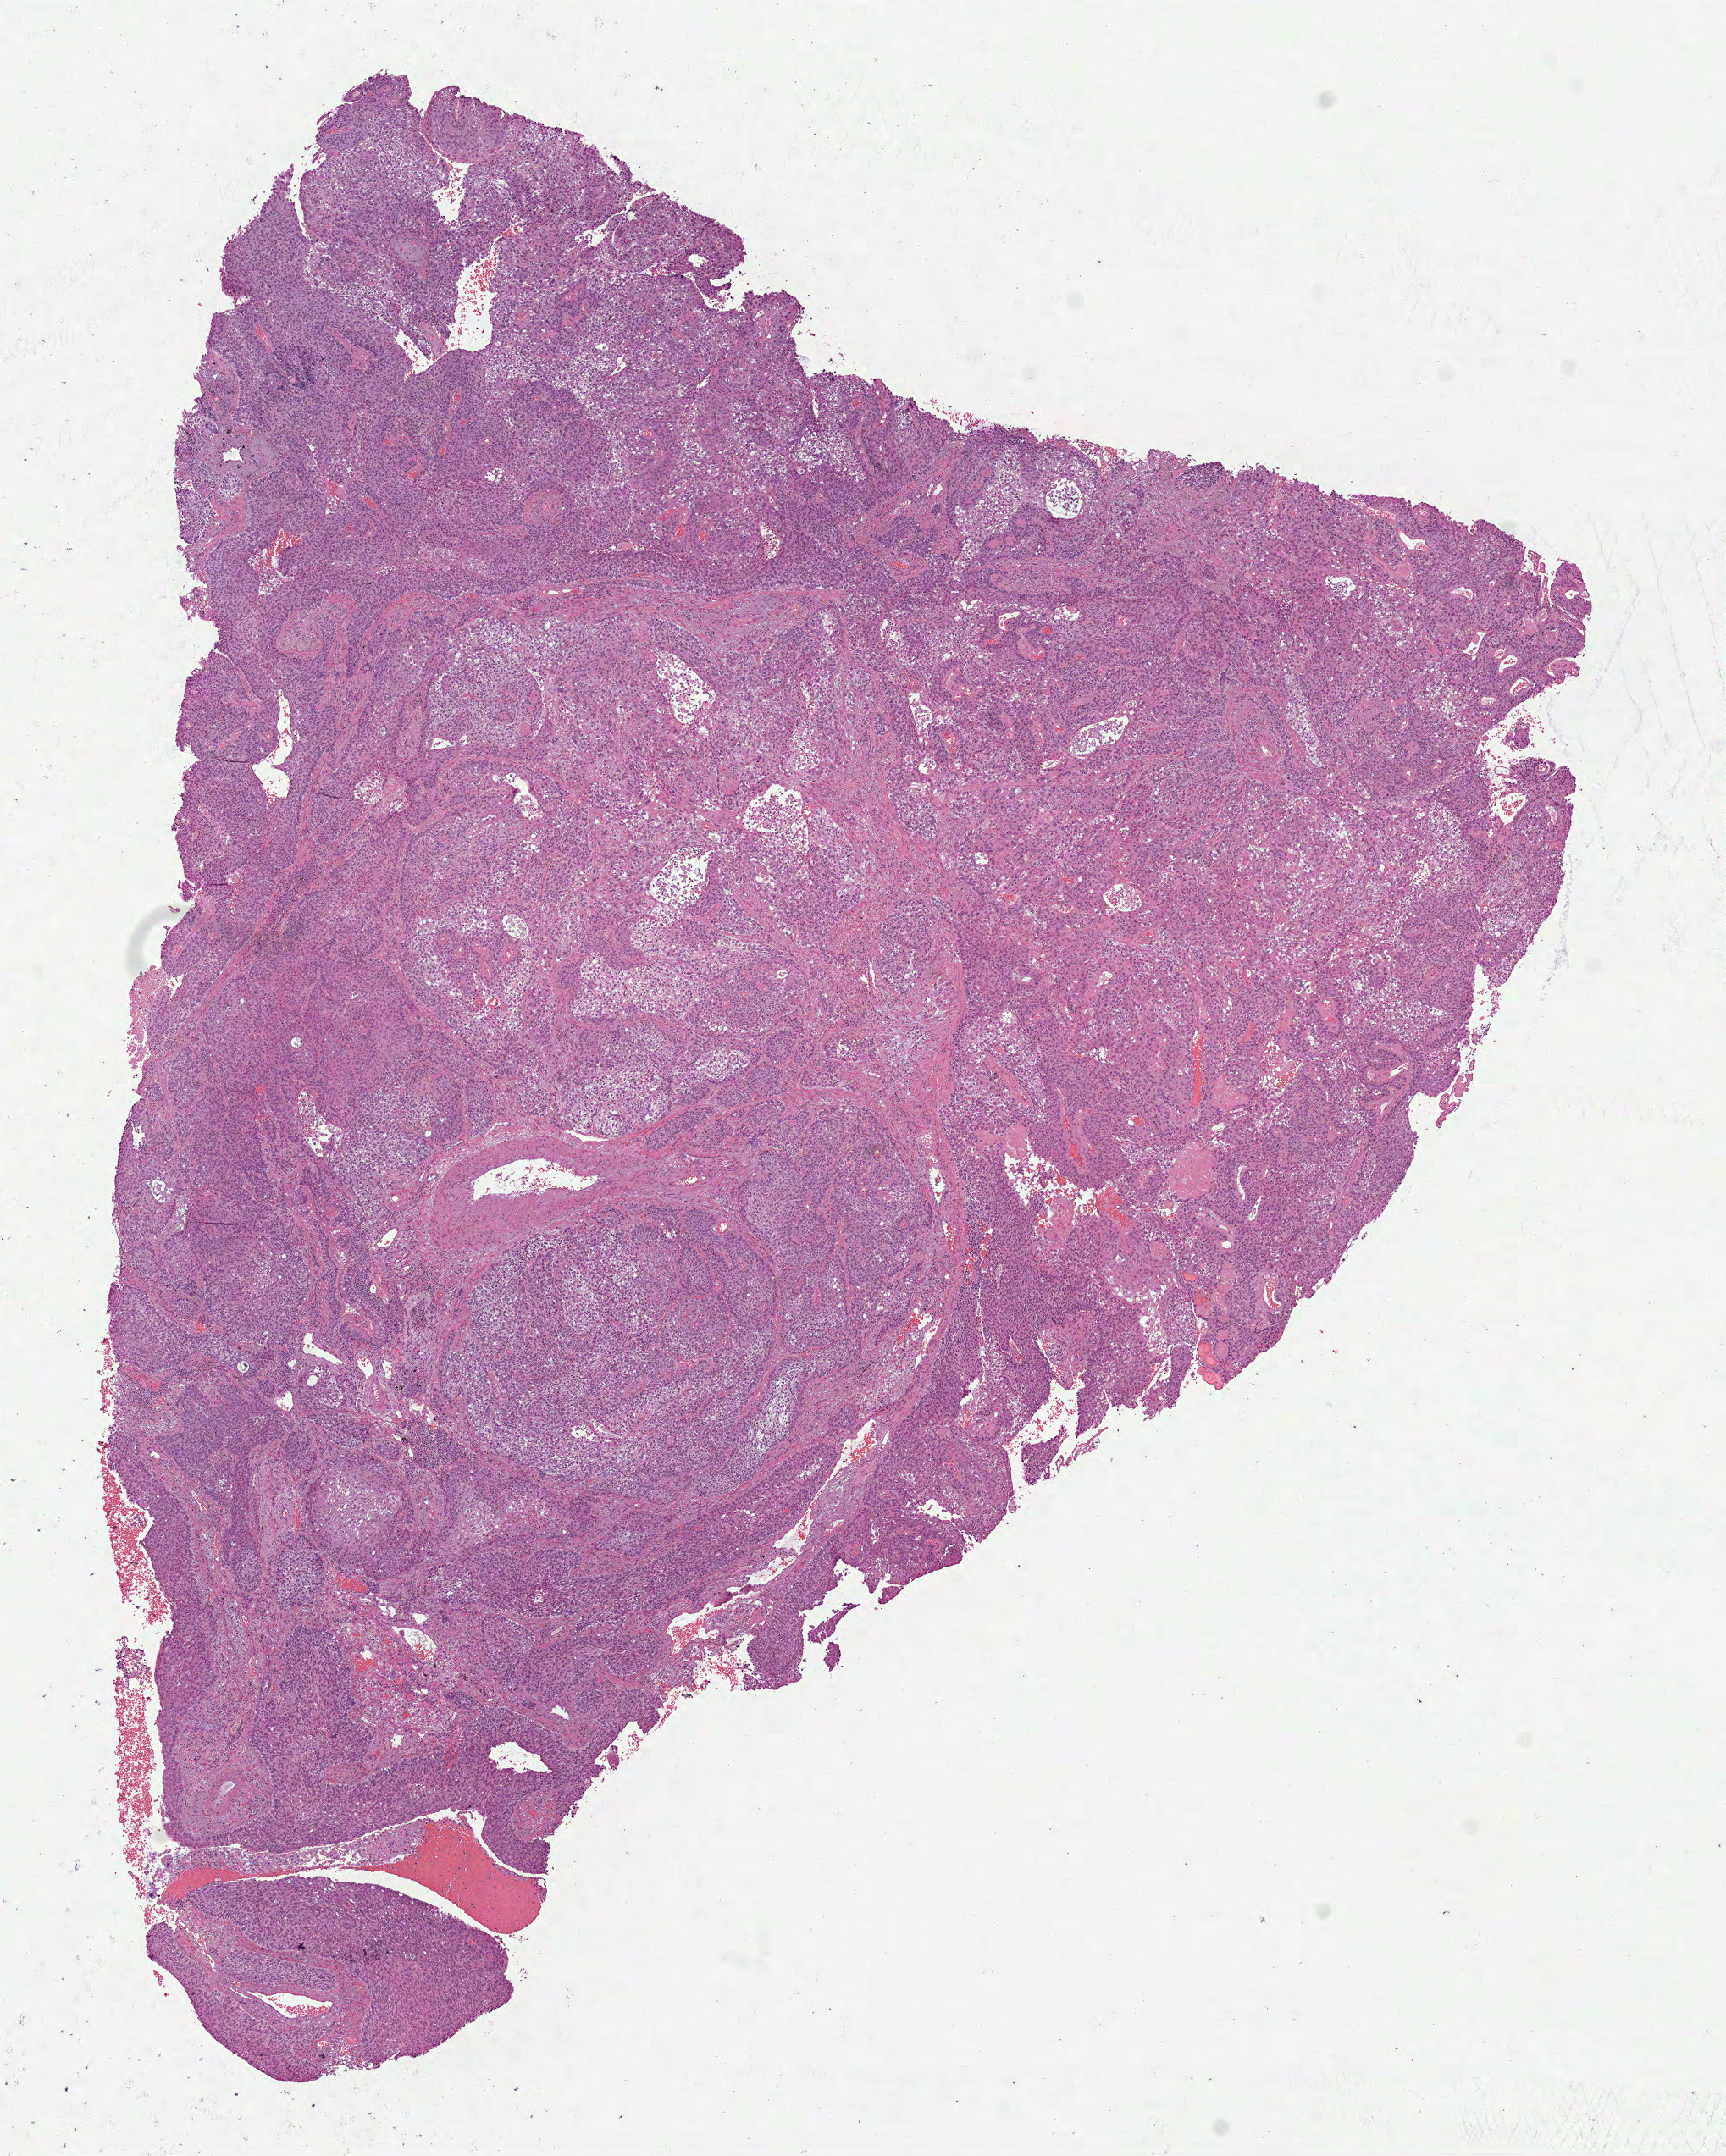
Digitized H&E-stained tissue section (whole slide), whole scanned area (about 8.2 x 10.3 mm) shown as a low-resolution overview; FFPE section; primary tumour sample from the lung. Patient: male, age at initial diagnosis 70 years.
Diagnosis: Squamous cell carcinoma, NOS (lower lobe, lung). AJCC pathologic stage: IIA (7th edition). Laterality: right. TNM: T2b N0 MX.